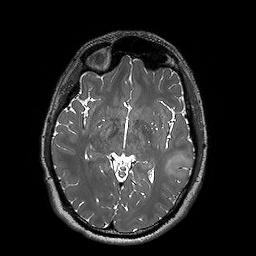
Brain MRI from a brain-tumour surgery series, one axial slice. Slice 94 of 192 in the series (ordered by position). 1 mm slice thickness. 256 × 256 image matrix, field of view 250 × 250 mm. Case-level facts recorded for this patient, not image findings: histopathology: Oligodendroglioma; WHO grade: 2; IDH mutation: yes.
Annotated regions visible in this slice (outlined manually by an expert reader):
- tumour: bounding box [x1, y1, x2, y2] px = [159, 155, 193, 182]